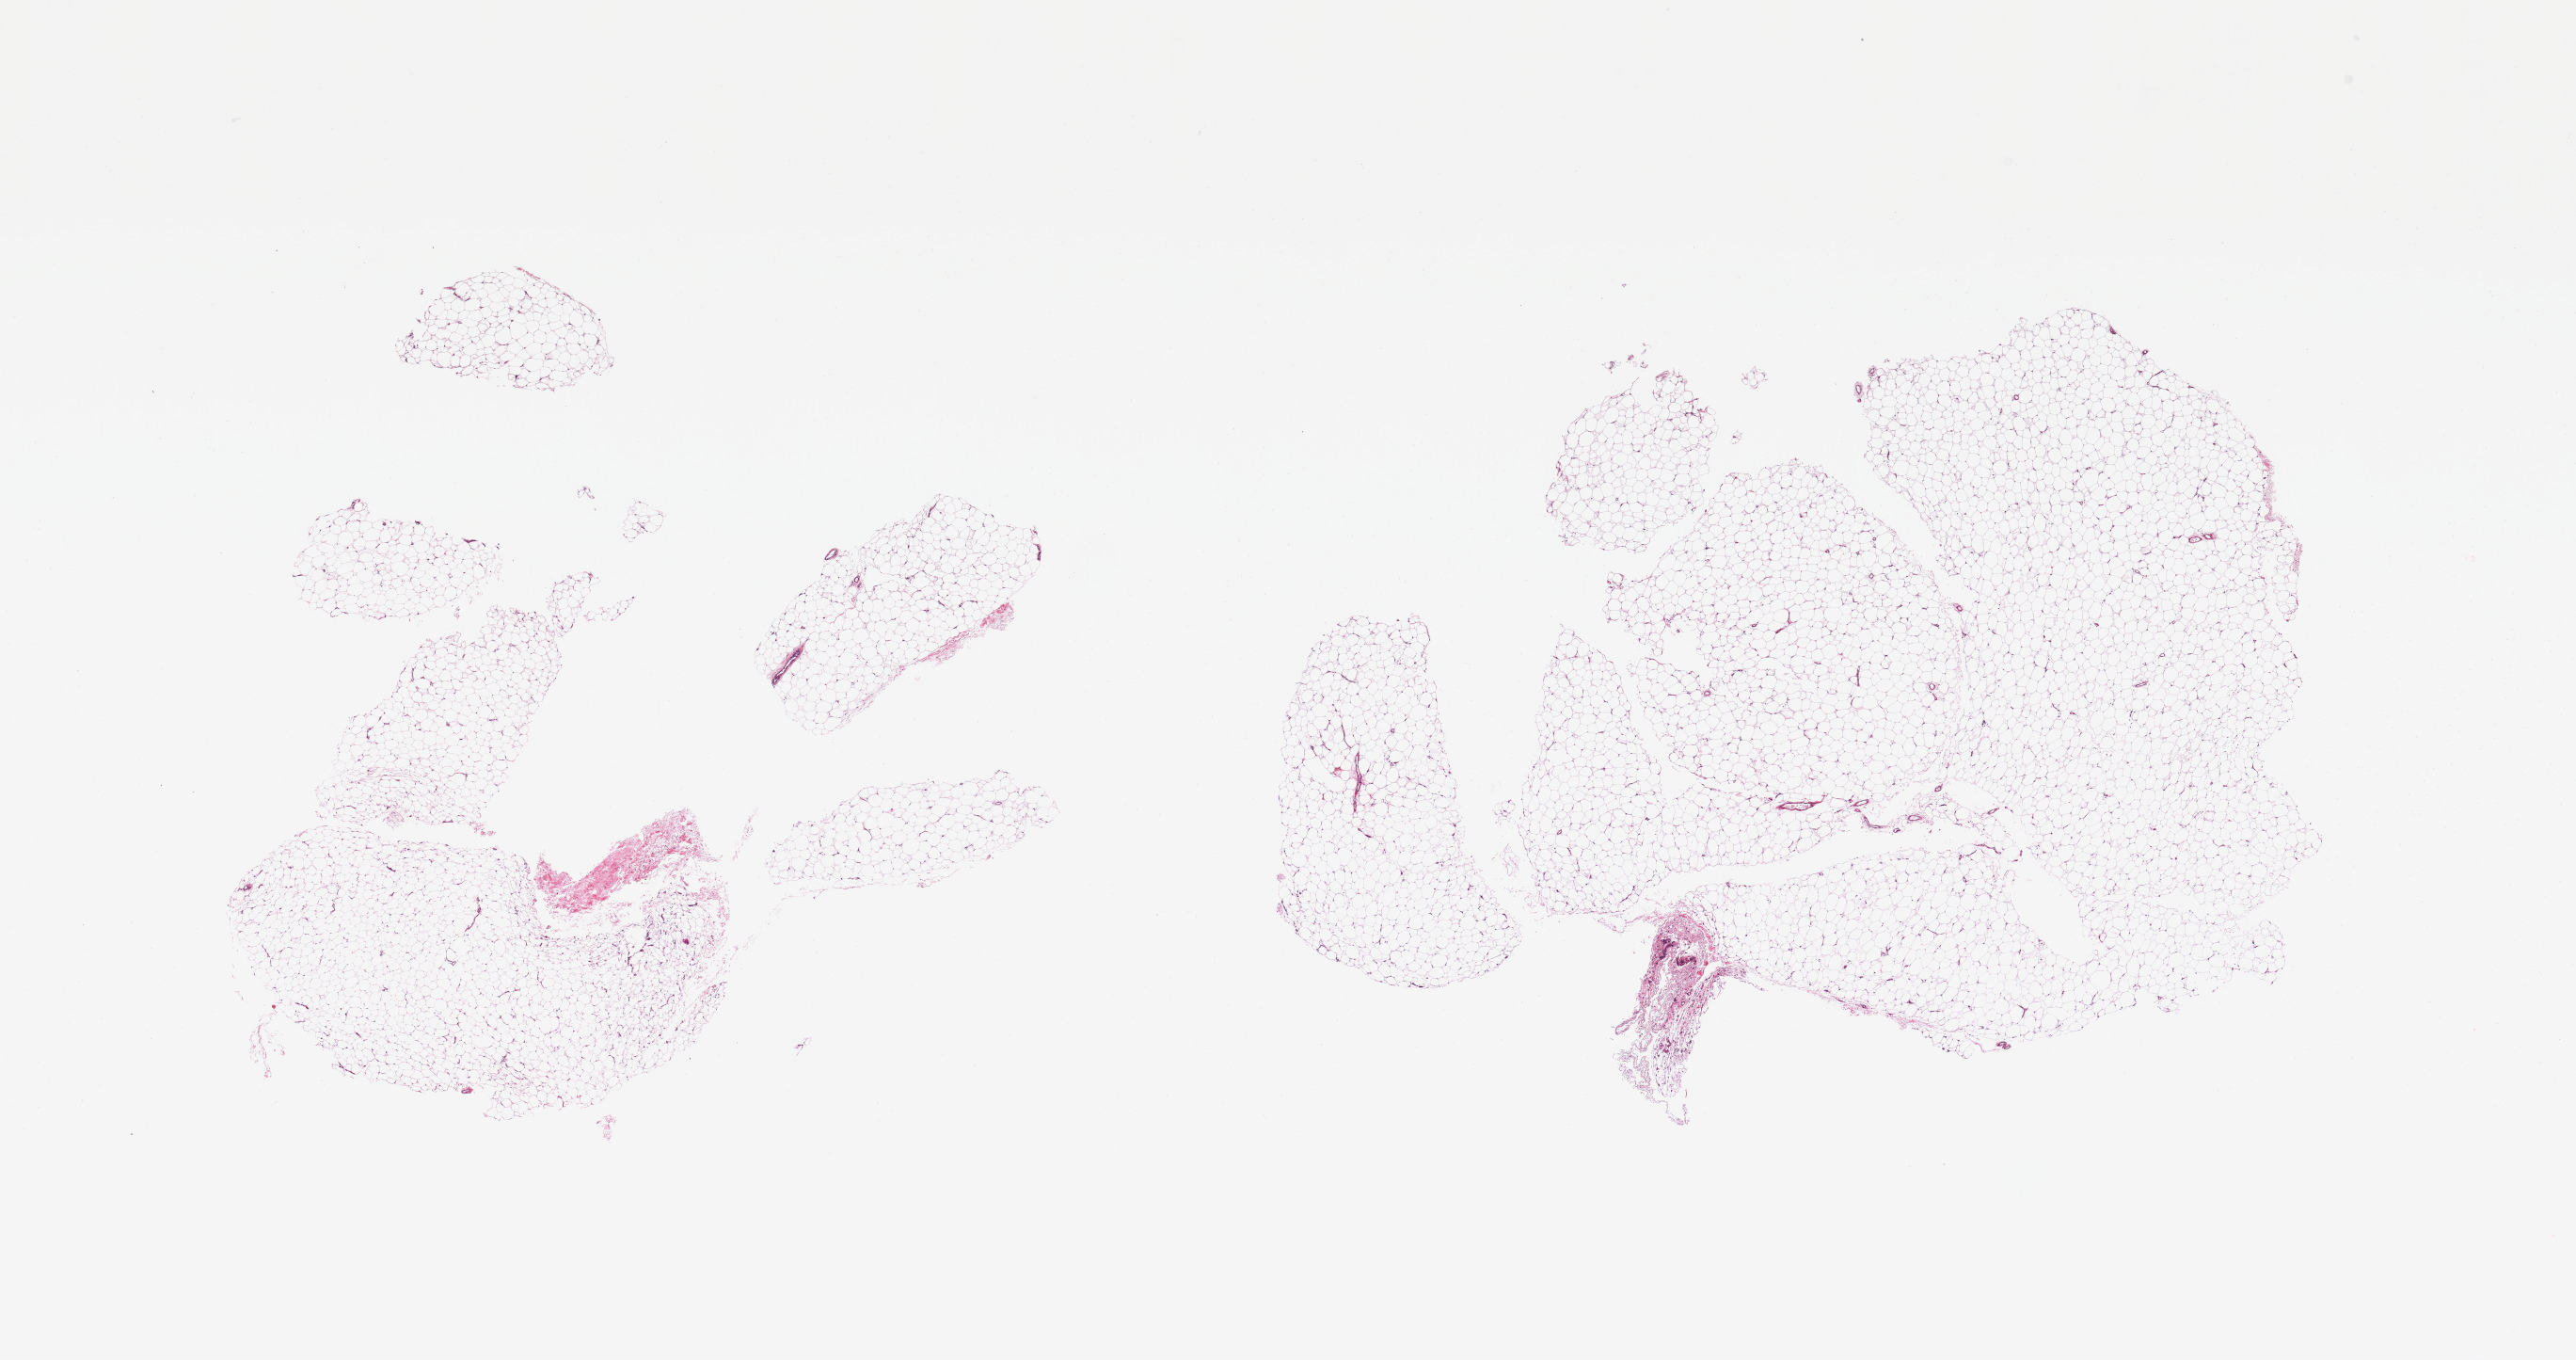
Whole-slide image, H&E stain, shown as a low-resolution overview of the whole scanned area (about 21.7 x 11.4 mm, acquisition: 20x scan). PAXgene-fixed paraffin-embedded (PFPE) section. Sampled site (target tissue): adipose tissue. Donor tissue sample. Female donor.
Pathologist's review note for this sample: 2 pieces; minimal fibrous content.